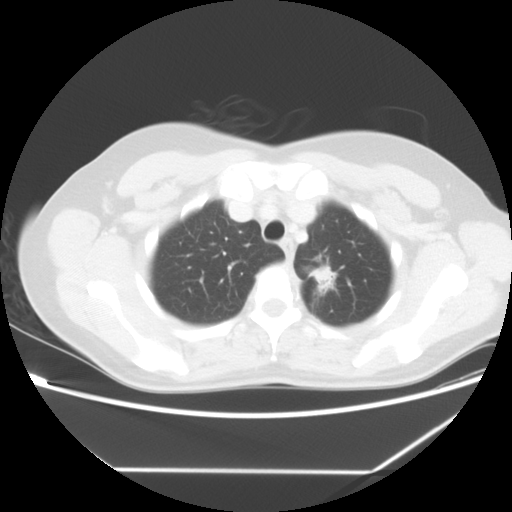
Chest CT, one axial slice. Position 49 of 60 along the scan axis. 140 kVp. Lung window (W 1500 / L -600 HU). 5 mm slice thickness. 512 × 512 image matrix, field of view 367 × 367 mm. Patient: female, 43 years. From the clinical record (not read from this slice): clinical TNM (as recorded): T1c N0 M1b.
Annotated regions visible in this slice (rectangle marked by the reading radiologist):
- lung tumour (recorded histology: adenocarcinoma): bounding box [x1, y1, x2, y2] px = [310, 259, 342, 297]